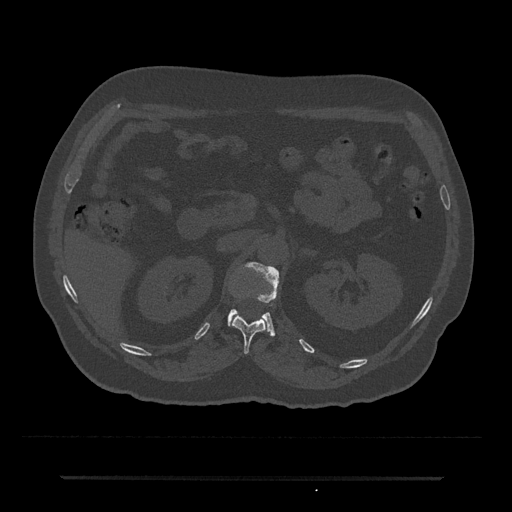
CT including the spine, one axial slice. Slice 105 of 797 in the series (ordered by position). Bone window (W 1800 / L 400 HU). 0.5 mm slice thickness. 512 × 512 image matrix. Male patient, age 69 years. Case-level facts recorded for this patient, not image findings: primary cancer: prostate.
Annotated regions visible in this slice (semi-automatic segmentation, software-assisted and operator-edited):
- L1 vertebra: bounding box (x1, y1, x2, y2) in pixels: (227, 263, 279, 335)
- T12 vertebra: (232, 313, 268, 354)